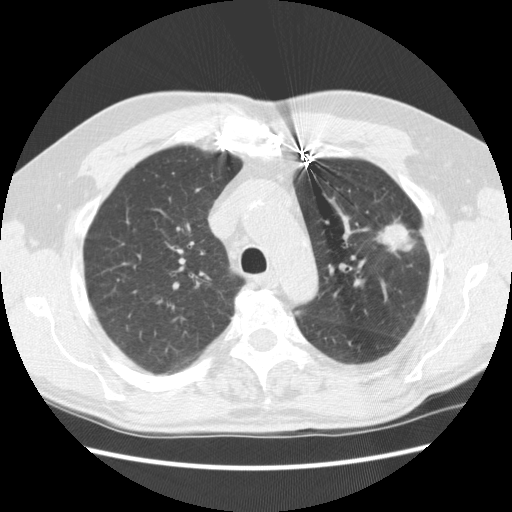
Chest CT (low-dose screening protocol), one axial image. Baseline annual screen. Lung window (W 1500 / L -600 HU). Slice 176 of 231 in the series. 512 × 512 image matrix. Male, age 72 years at enrolment. Former smoker at enrolment.
Lesion marked by an expert reader, bounding box (x1, y1, x2, y2) in pixels: (348, 199, 428, 260). Reader record for this screening exam (exam-level; its link to the box is not recorded): non-calcified nodule or mass ≥4 mm, left upper lobe, 25 × 18 mm, spiculated (stellate) margins, soft tissue attenuation. Official screen result: positive, change unspecified: nodule(s) >= 4 mm or enlarging nodule(s), mass(es), or other non-specific abnormalities suspicious for lung cancer.